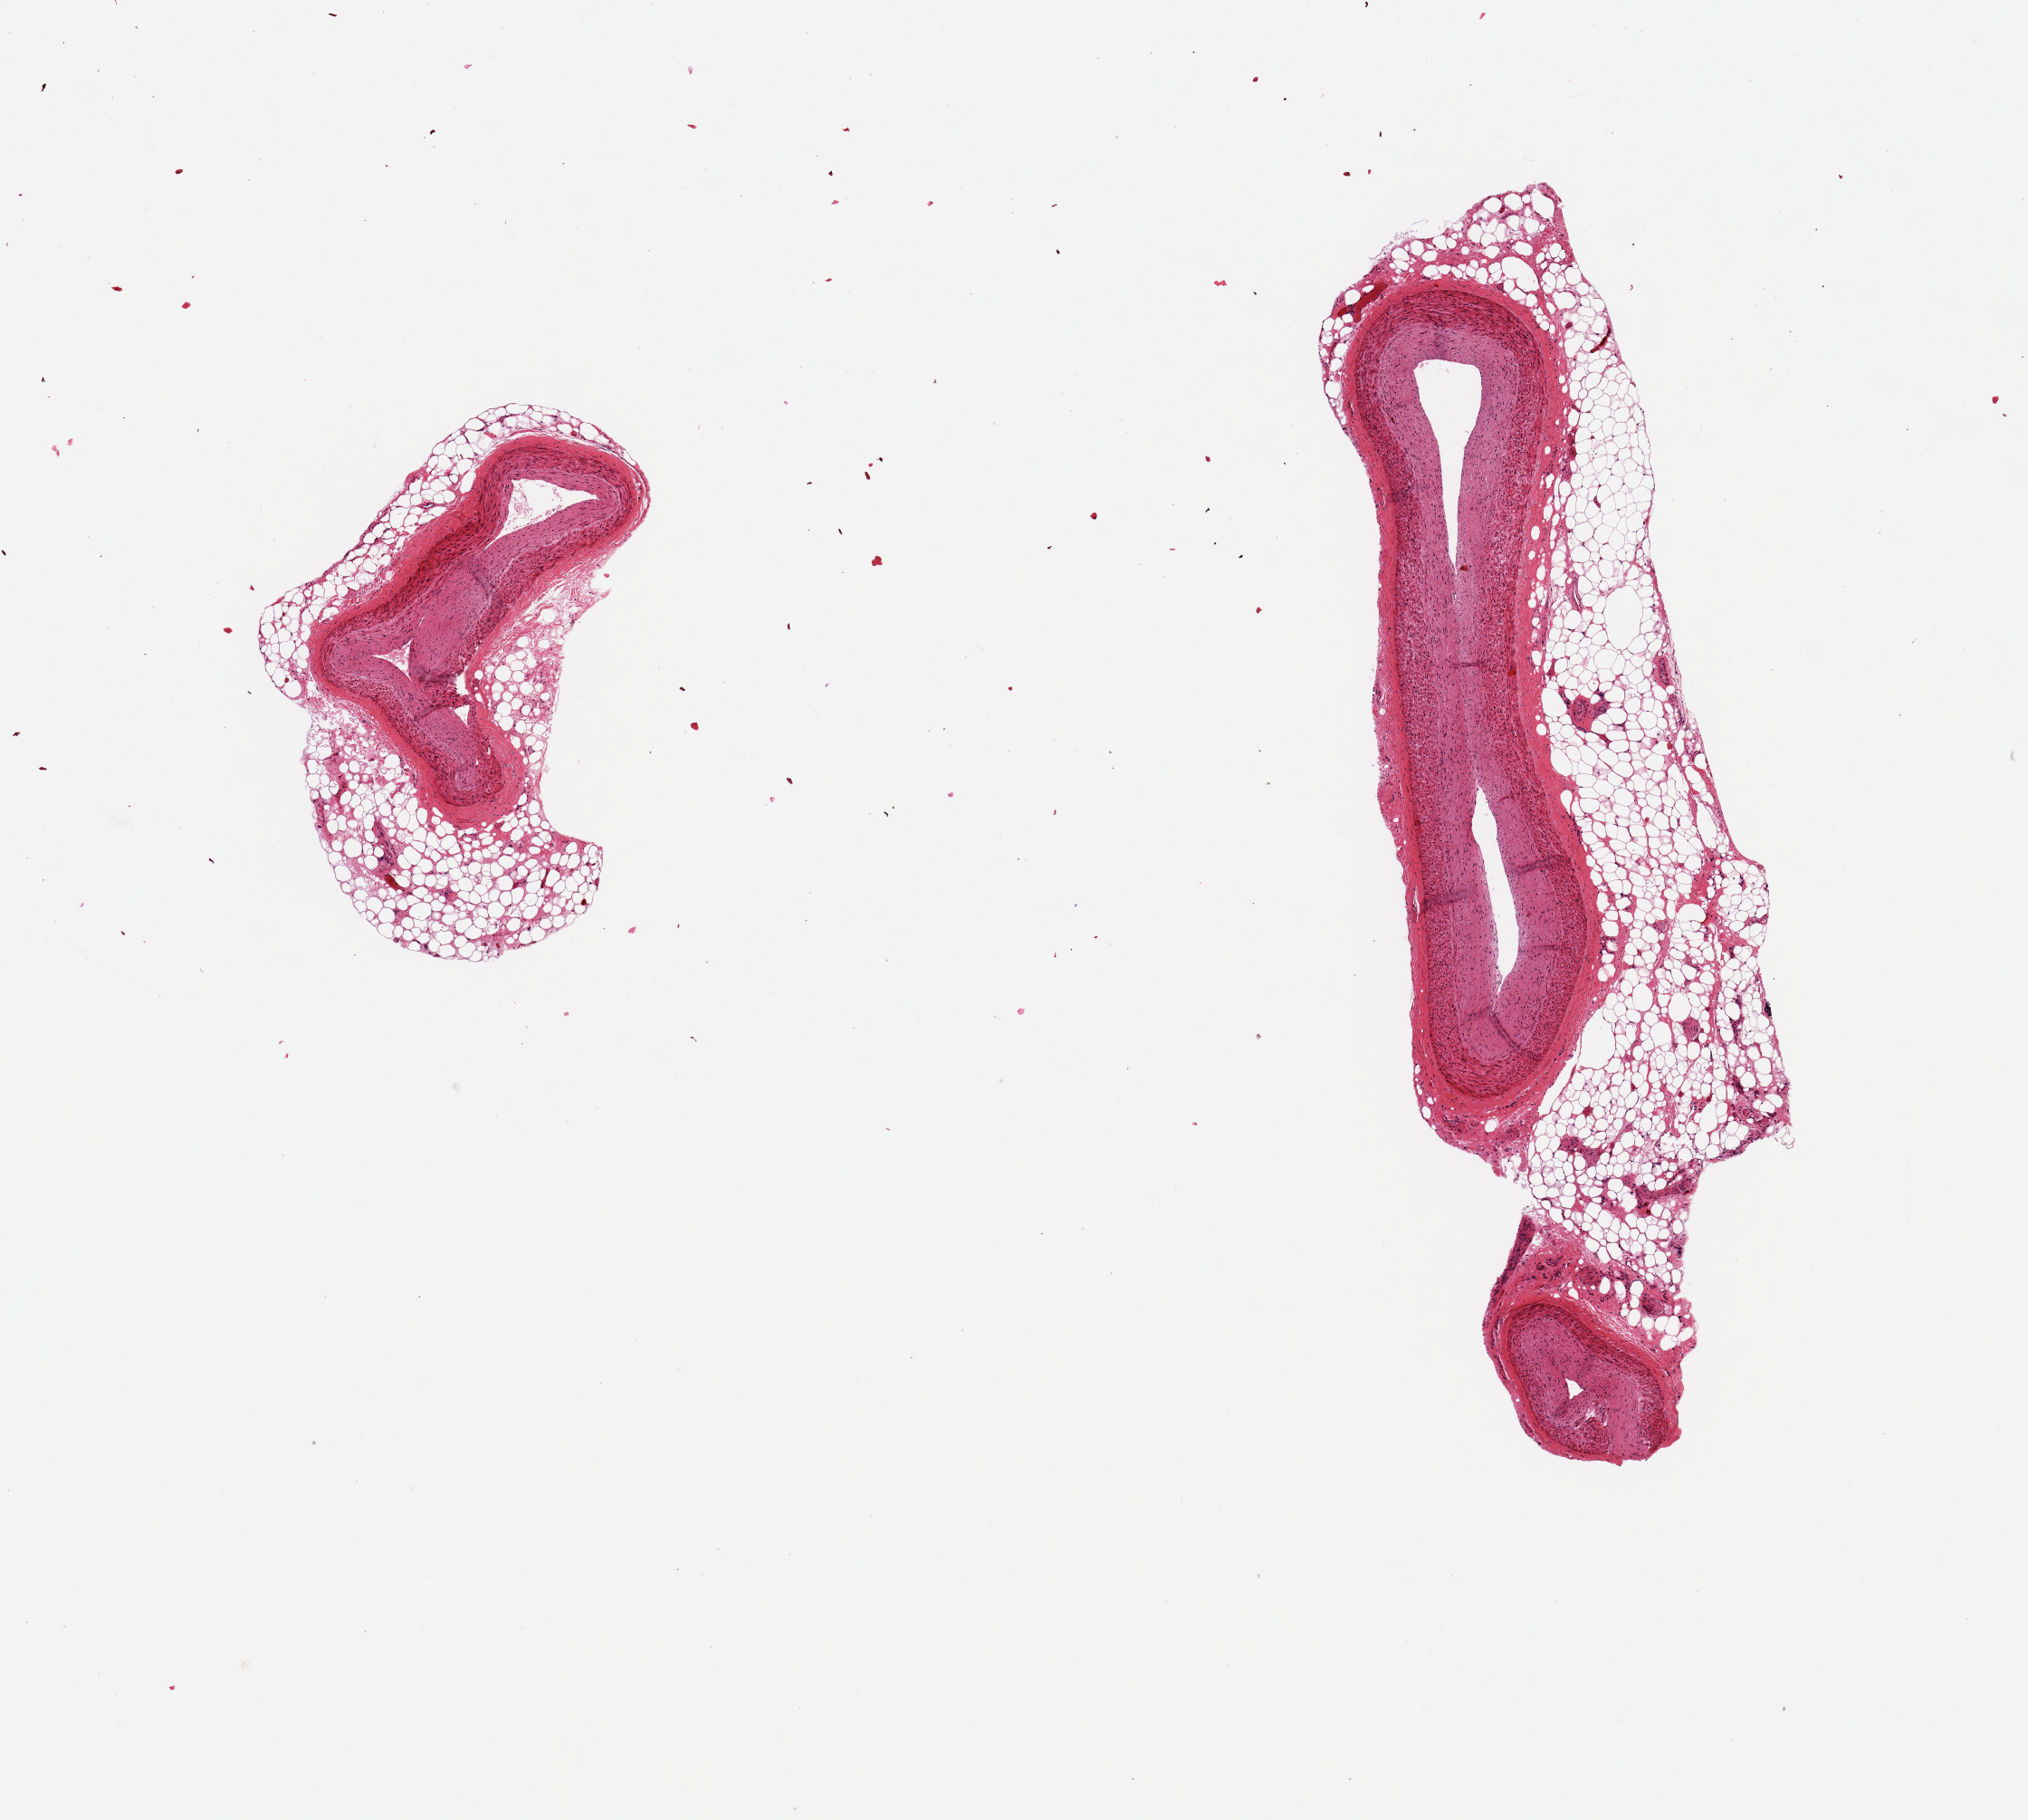
Whole-slide image, hematoxylin and eosin (H&E) stain — low-resolution overview of the scanned area, about 8.9 x 7.9 mm (acquisition: 20x scan), PAXgene-fixed paraffin-embedded (PFPE) section, section of coronary artery (target tissue), donor tissue sample. Donor sex: female.
Reviewer comment on this tissue sample: 1 pieces ~1.5-2mm d. ~0.5-1 mm adherent fat encircles both.